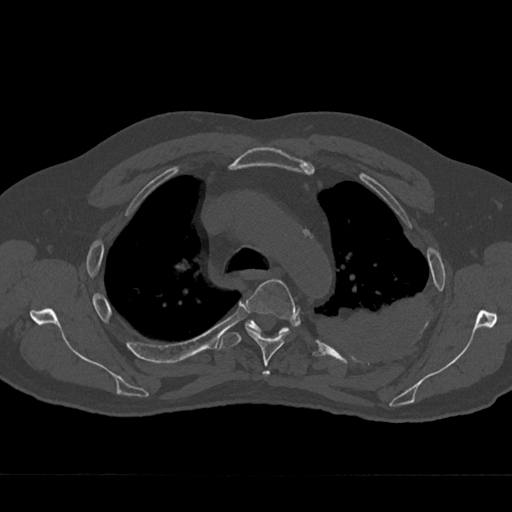
CT including the spine, one axial slice. Position 507 of 797 along the scan axis. 120 kVp. Bone window (W 1800 / L 400 HU). 0.5 mm slice thickness. 512 × 512 image matrix, field of view 377 × 377 mm. Male patient, age 75 years. Case-level facts recorded for this patient, not image findings: primary cancer: renal.
Outlined on this slice (semi-automatically segmented with operator editing):
- T3 vertebra: bounding box <263,371,270,375> (left, top, right, bottom; pixels)
- T4 vertebra: <245,279,296,376>
- T5 vertebra: <220,320,289,349>